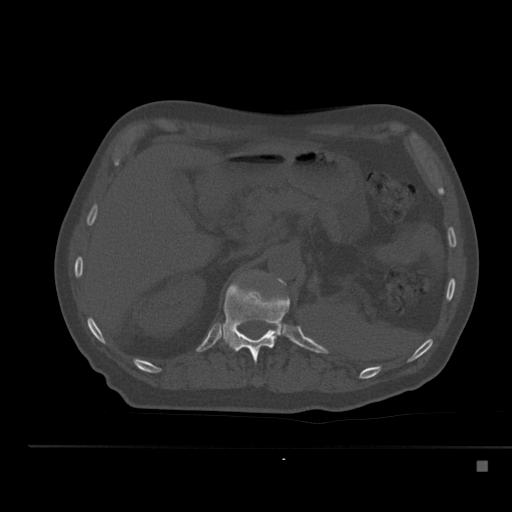
CT including the spine, one axial slice; position 227 of 517 along the scan axis; 120 kVp; bone window (W 1800 / L 400 HU); 512 × 512 image matrix, field of view 408 × 408 mm. Patient: male, 70 years. Case-level facts recorded for this patient, not image findings: primary cancer: renal; vertebrae with lytic lesions (as recorded): T4, T6, T10, T12, L3, L4, L5.
Outlined on this slice (semi-automatic segmentation, software-assisted and operator-edited):
- L1 vertebra: bounding box <277,278,285,284> (left, top, right, bottom; pixels)
- T12 vertebra: <222,281,290,363>